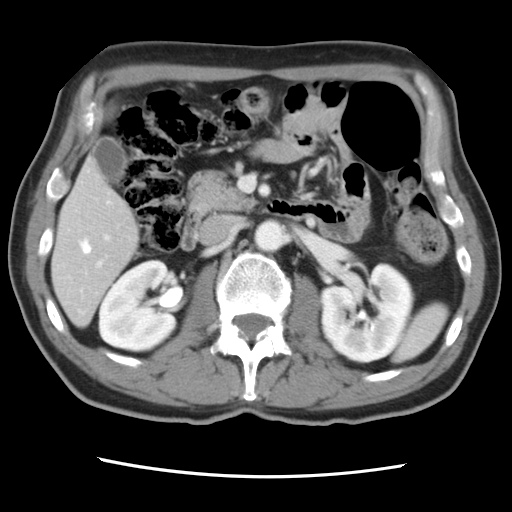
Contrast-enhanced abdominal CT, one axial slice; position 35 of 83 along the scan axis; intravenous contrast given; soft-tissue window (W 400 / L 40 HU); 512 × 512 image matrix, field of view 321 × 321 mm. Male patient, age 69 years. From the clinical record (not read from this slice): diagnosis: colorectal cancer liver metastases, imaged before liver resection; multiple liver metastases: yes; largest metastasis: 3.5 cm; chemotherapy before resection: yes.
Outlined on this slice (expert manual segmentation):
- hepatic veins: box from (x=80, y=239) to (x=92, y=254) px
- liver: (x=52, y=162)–(x=139, y=325)
- planned liver remnant (the part of the liver to remain after resection): (x=52, y=162)–(x=139, y=325)
- portal vein (with intrahepatic branches): (x=80, y=234)–(x=110, y=293)